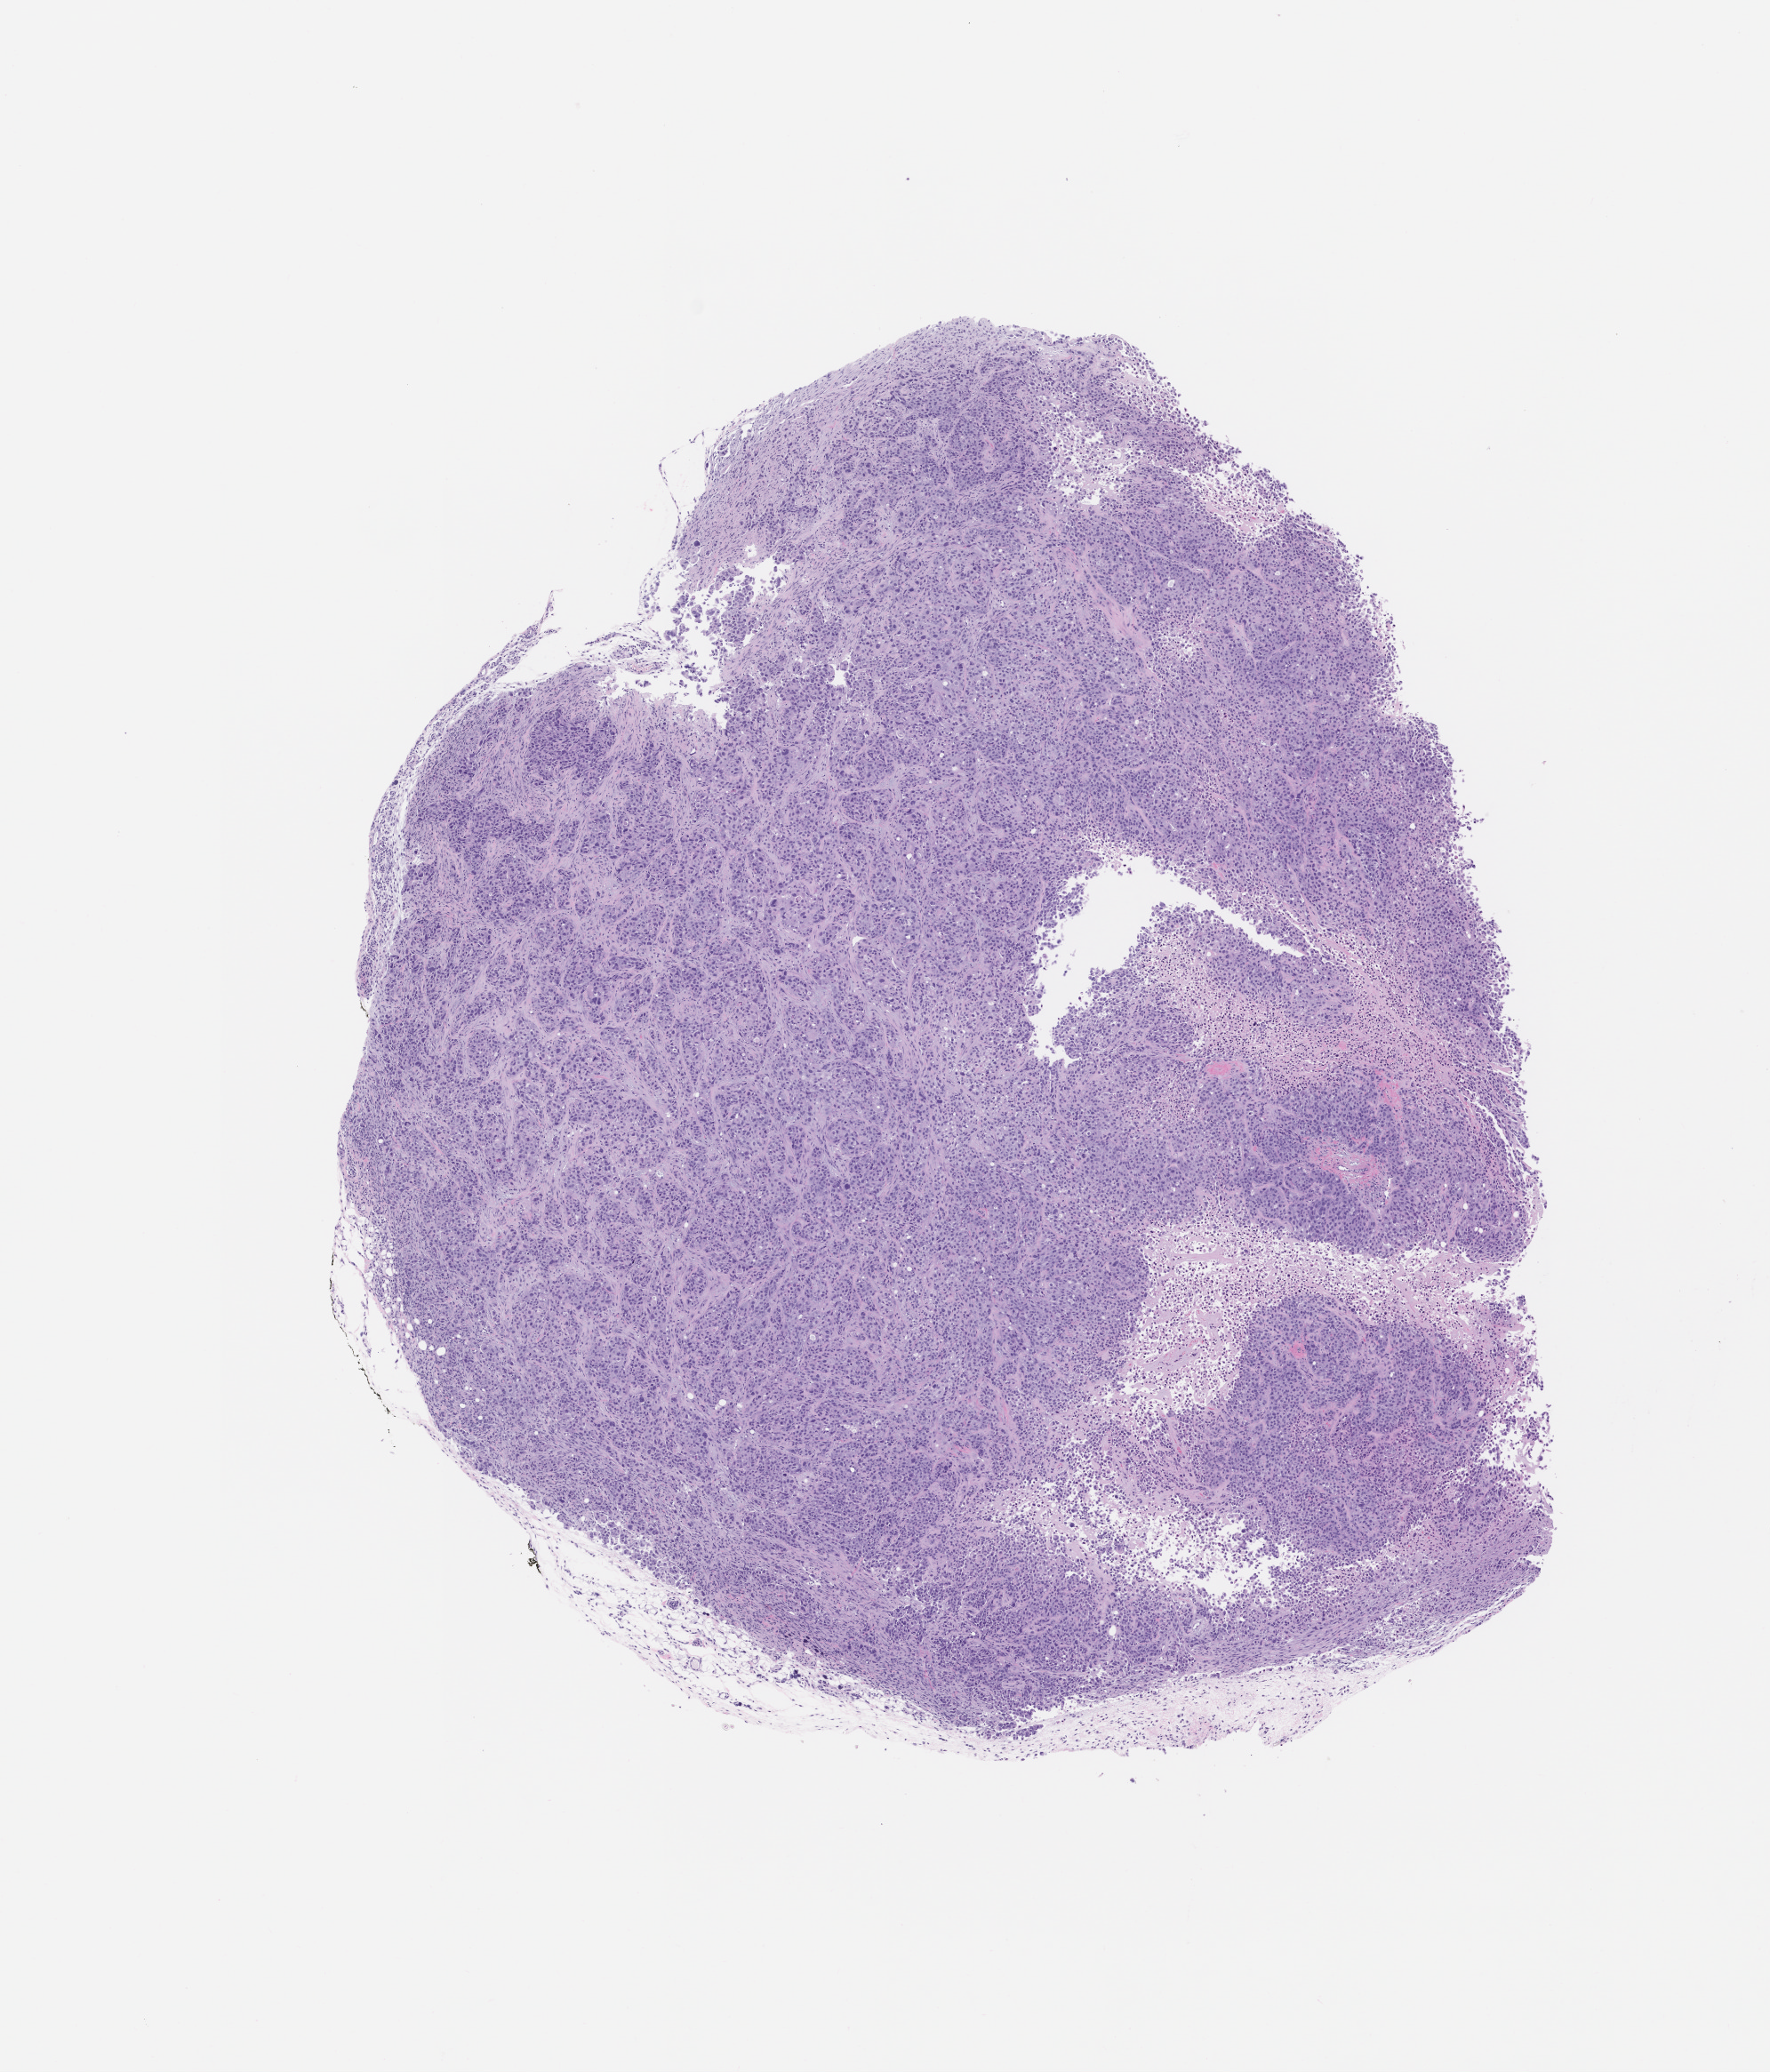
Whole-slide image, haematoxylin and eosin: patient-derived xenograft (human tumor grown in a mouse), passage 1 — shown as a low-resolution overview of the whole scanned area (about 8.0 x 9.3 mm), FFPE section, tumor site category: lung.
* originating patient diagnosis: Lung Adenocarcinoma